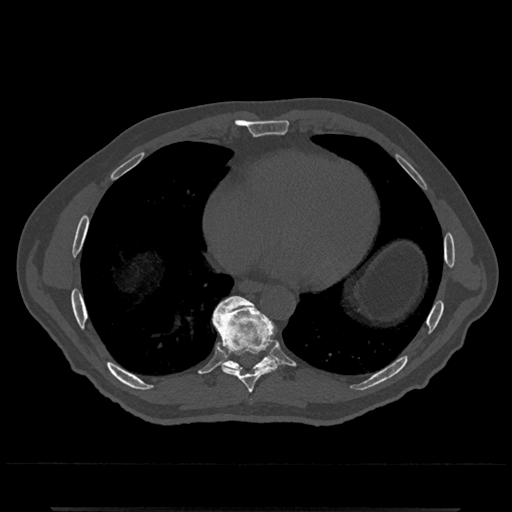
CT including the spine, one axial slice; slice 648 of 797 in the series (ordered by position); 120 kVp; bone window (W 1800 / L 400 HU); 0.5 mm slice thickness; 512 × 512 image matrix, field of view 393 × 393 mm. Patient: male, 67 years. From the clinical record (not read from this slice): primary cancer: prostate.
Annotated regions visible in this slice (semi-automatically segmented with operator editing):
- T8 vertebra: bounding box [x1, y1, x2, y2] px = [213, 306, 280, 393]
- T9 vertebra: [212, 295, 277, 371]